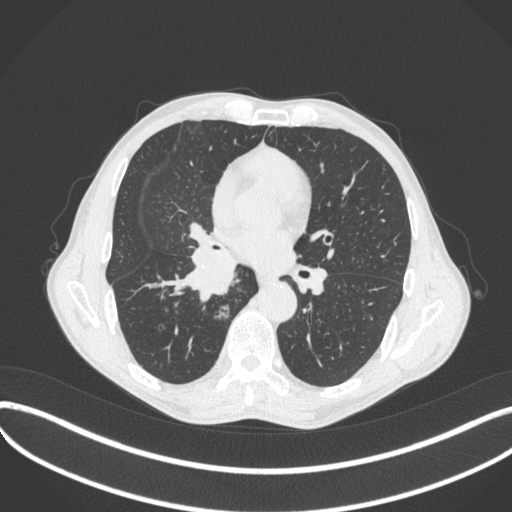
Chest CT, one axial slice; position 220 of 481 along the scan axis; reconstruction kernel B31f; 120 kVp; lung window (W 1500 / L -600 HU); 1 mm slice thickness; 512 × 512 image matrix, field of view 400 × 400 mm. Patient: male, 65 years. From the clinical record (not read from this slice): clinical TNM (as recorded): T2a N0 M0; histopathological grade: G2.
Outlined on this slice (bounding box drawn by a radiologist):
- lung tumour (recorded histology: squamous cell carcinoma): bounding box (x1, y1, x2, y2) in pixels: (176, 239, 237, 304)